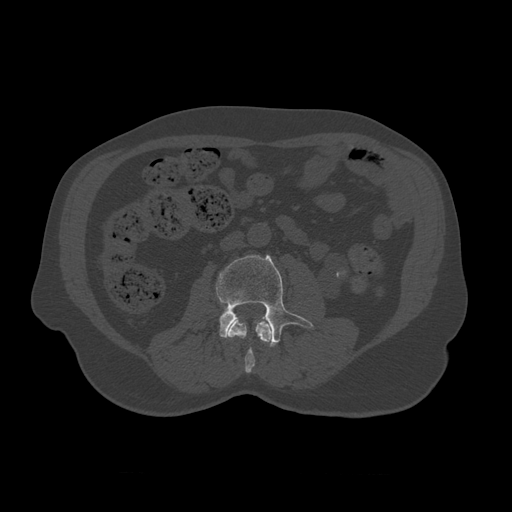
CT including the spine, one axial slice. Position 312 of 450 along the scan axis. Reconstruction kernel STANDARD. 120 kVp. Bone window (W 1800 / L 400 HU). 512 × 512 image matrix, field of view 405 × 405 mm. Patient age 75 years. From the clinical record (not read from this slice): primary cancer: prostate.
Outlined on this slice (semi-automatic segmentation, software-assisted and operator-edited):
- L2 vertebra: bounding box (x1, y1, x2, y2) in pixels: (227, 317, 273, 374)
- L3 vertebra: (216, 255, 314, 348)